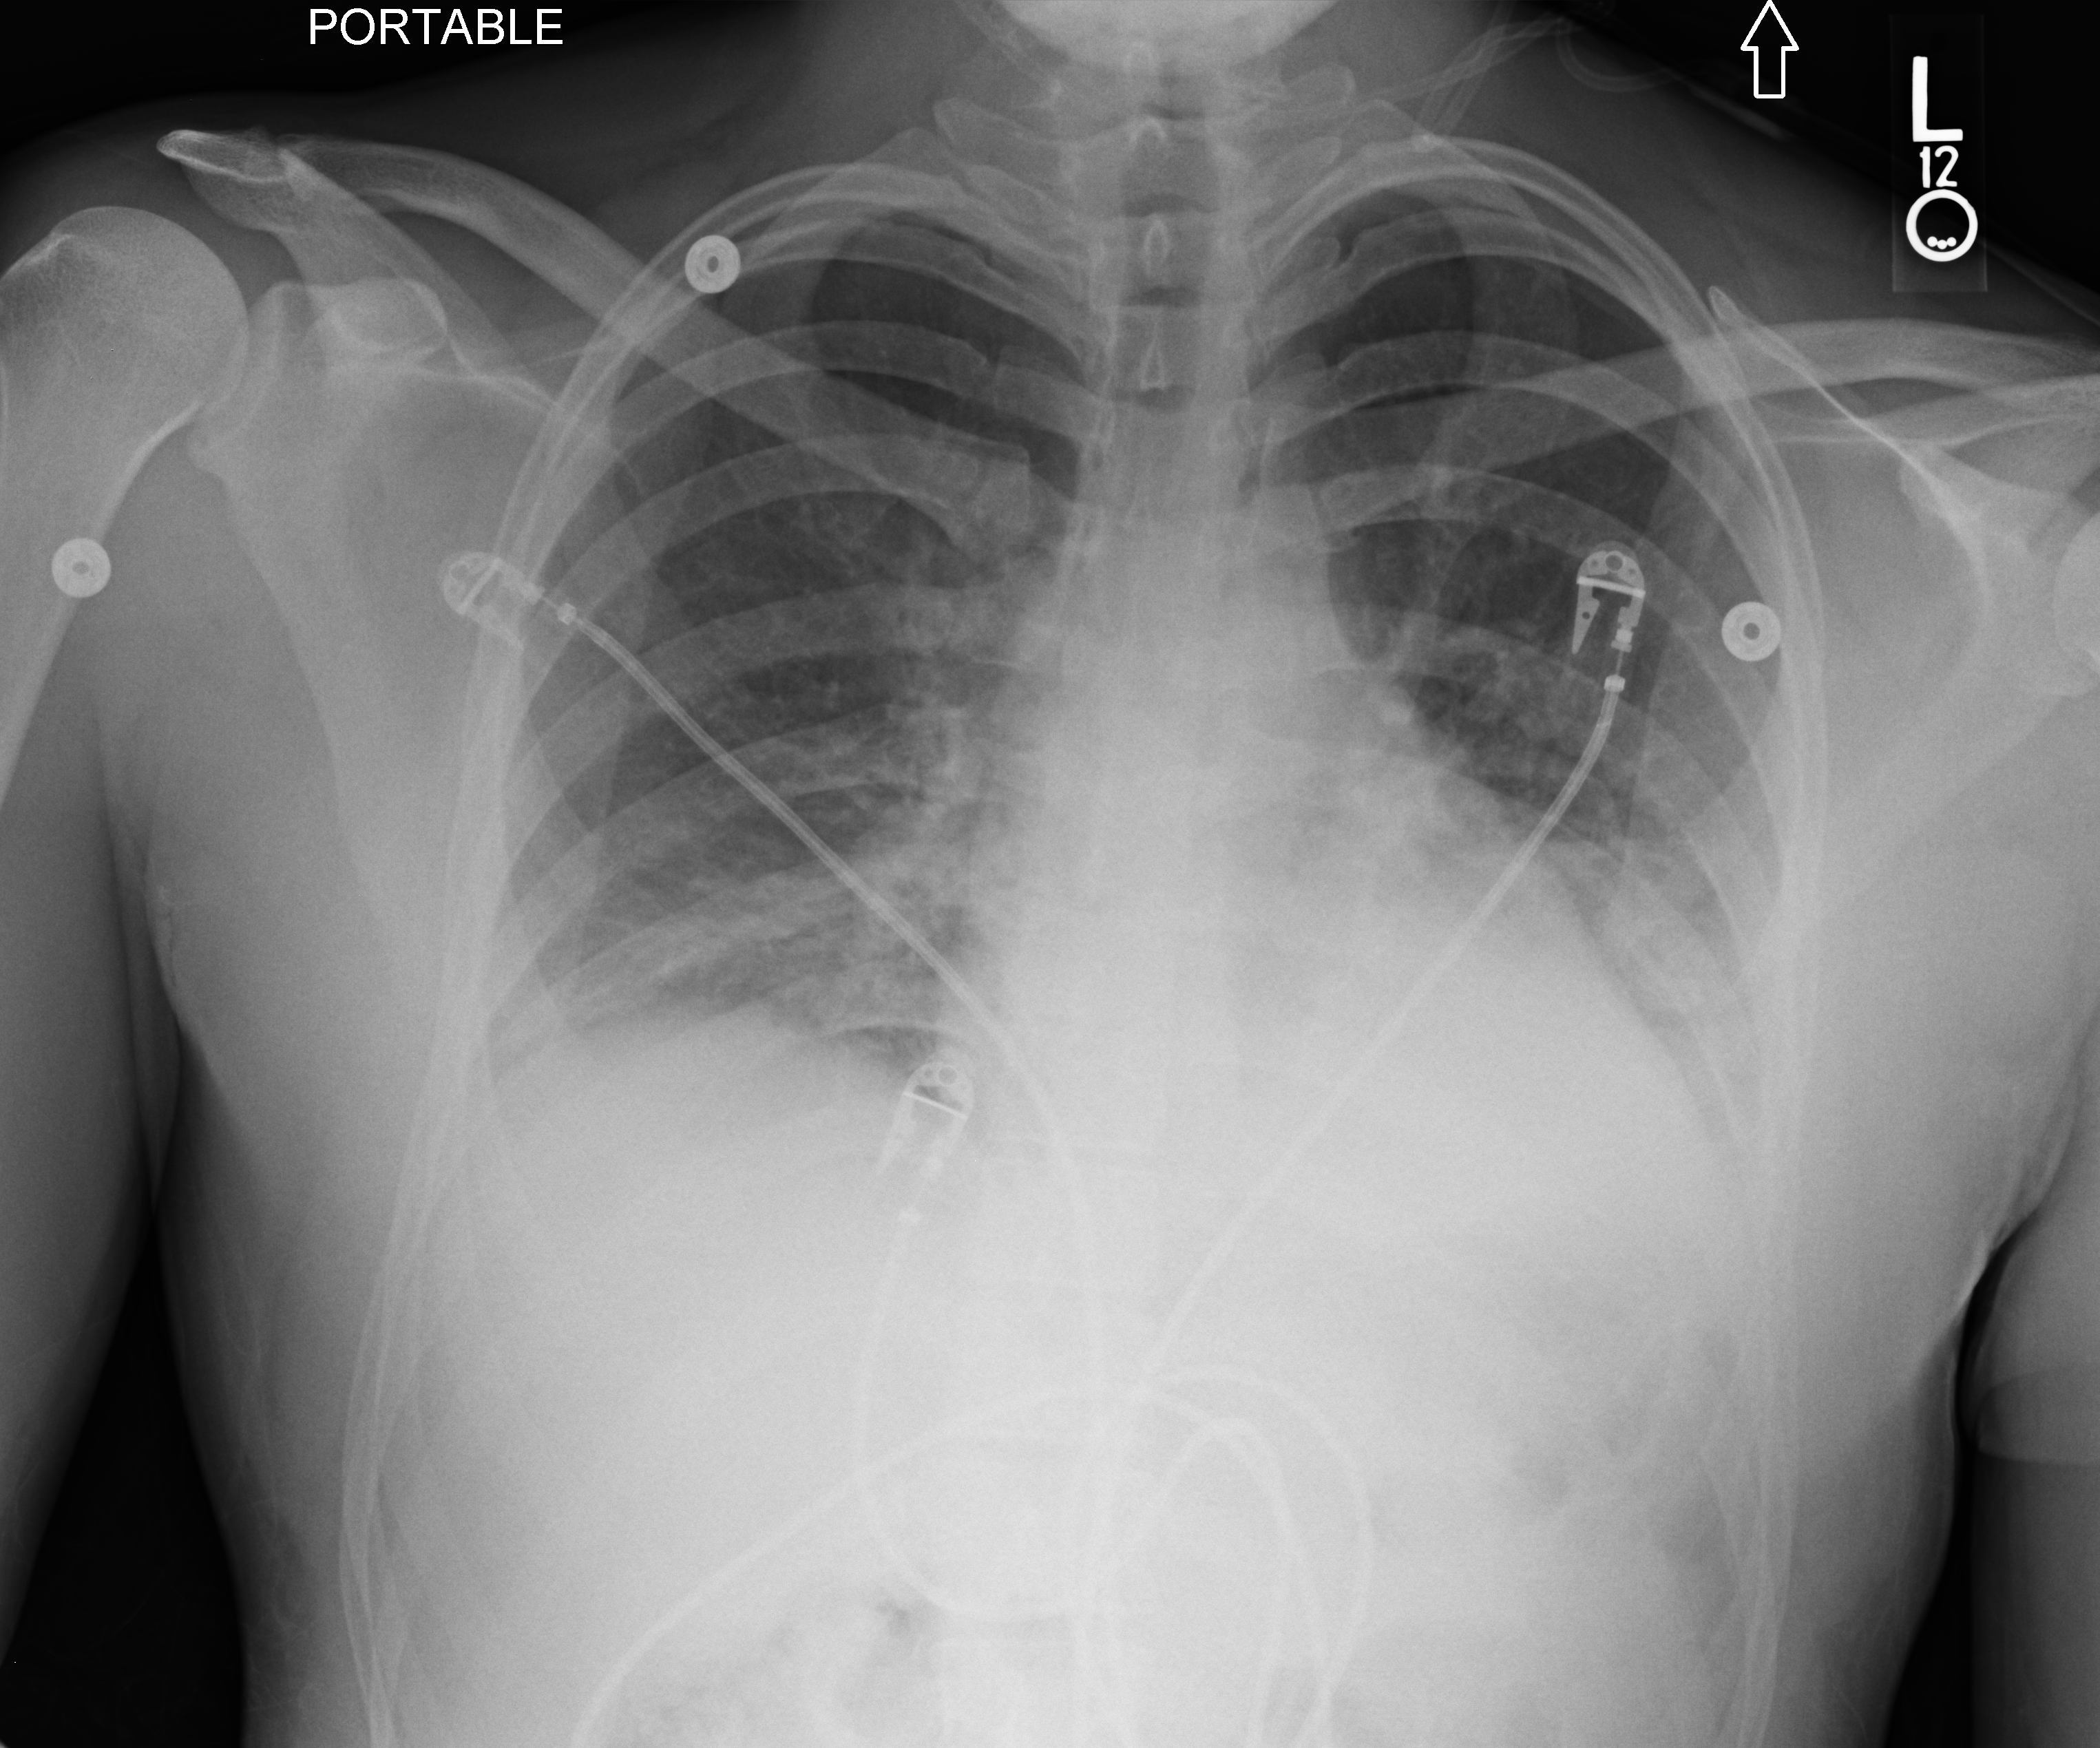
Bedside chest radiograph (computed radiography); anteroposterior (AP) projection. Patient hospitalised with COVID-19; male, aged 18–59 years.
From the hospital-stay record, not from the radiograph (when in the stay this image was taken is not recorded):
- admitted to intensive care during this hospital stay: no